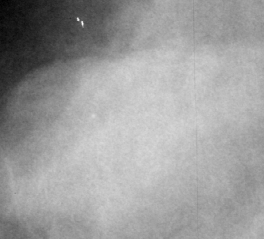
Crop from a digitized film mammogram around one marked abnormality, right breast, CC view.
Finding: mass, shape lobulated, margins circumscribed / ill defined; BI-RADS assessment category 4; pathology result (as recorded, not read from the image): benign.